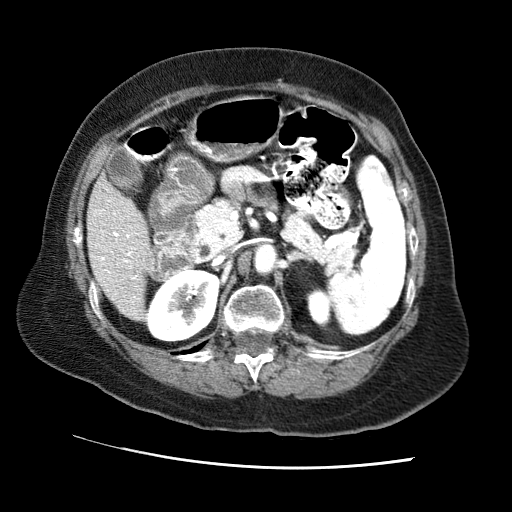
Contrast-enhanced abdominal CT (liver protocol), one axial slice. Position 25 of 65 along the scan axis. Reconstruction kernel STANDARD. 120 kVp. Soft-tissue window (W 400 / L 40 HU). 2.5 mm slice thickness. 512 × 512 image matrix. Case-level facts recorded for this patient, not image findings: diagnosis: hepatocellular carcinoma (patient treated with transarterial chemoembolisation; whether this scan precedes or follows treatment is not stated here); TNM stage (as recorded): Stage-II; Child-Pugh class: A; tumour differentiation: no biopsy.
Structures marked on this image (semi-automatically segmented with operator editing):
- liver parenchyma outside the tumour (the mass and vessels are separate outlines, so this box may not span the whole liver): bounding box (x1, y1, x2, y2) in pixels: (86, 175, 152, 320)
- liver vessels: (94, 210, 138, 300)